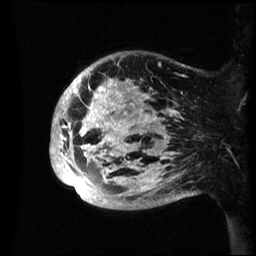
Breast MRI (dynamic contrast-enhanced), one sagittal slice. Position 11 of 60 along the scan axis. Dynamic contrast-enhanced series, image 2 of 3 at this slice position (ordered by acquisition). 1.5 T. TE 4.2 ms, TR 8.4 ms. 2.4 mm slice thickness. 256 × 256 image matrix. Patient: female, 48 years.
Outlined on this slice (semi-automatic segmentation, software-assisted and operator-edited):
- analysis volume of interest (the breast-tissue region the enhancement analysis was run in; not a lesion): box from (x=50, y=52) to (x=195, y=210) px
- tumour enhancement mask (voxels above the 70 % enhancement threshold inside the analysis volume of interest): (x=50, y=76)–(x=183, y=194)